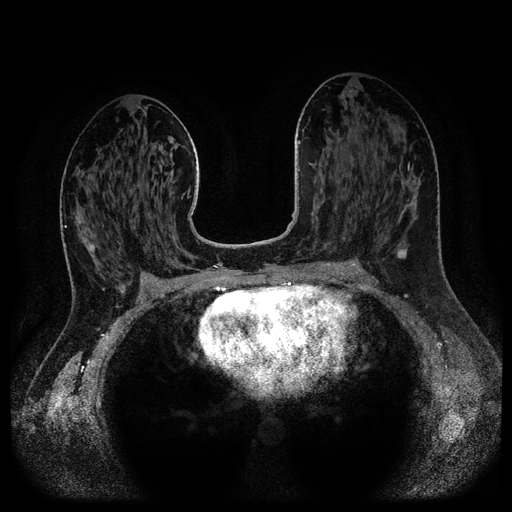
Breast MRI (dynamic contrast-enhanced, multi-phase), one axial slice. Dynamic contrast-enhanced series, time point 2 of 5 at this slice position (early post-contrast). 1.5 T. TE 2.6 ms, TR 5.3 ms. 2.1 mm slice thickness. 512 × 512 image matrix, field of view 360 × 360 mm. Female patient, age 37 years.
Outlined on this slice (semi-automatic segmentation, software-assisted and operator-edited):
- breast lesion (labelled 'tumour' in the annotation; benign lesions carry a separate 'benign' label): box from (x=396, y=248) to (x=408, y=259) px